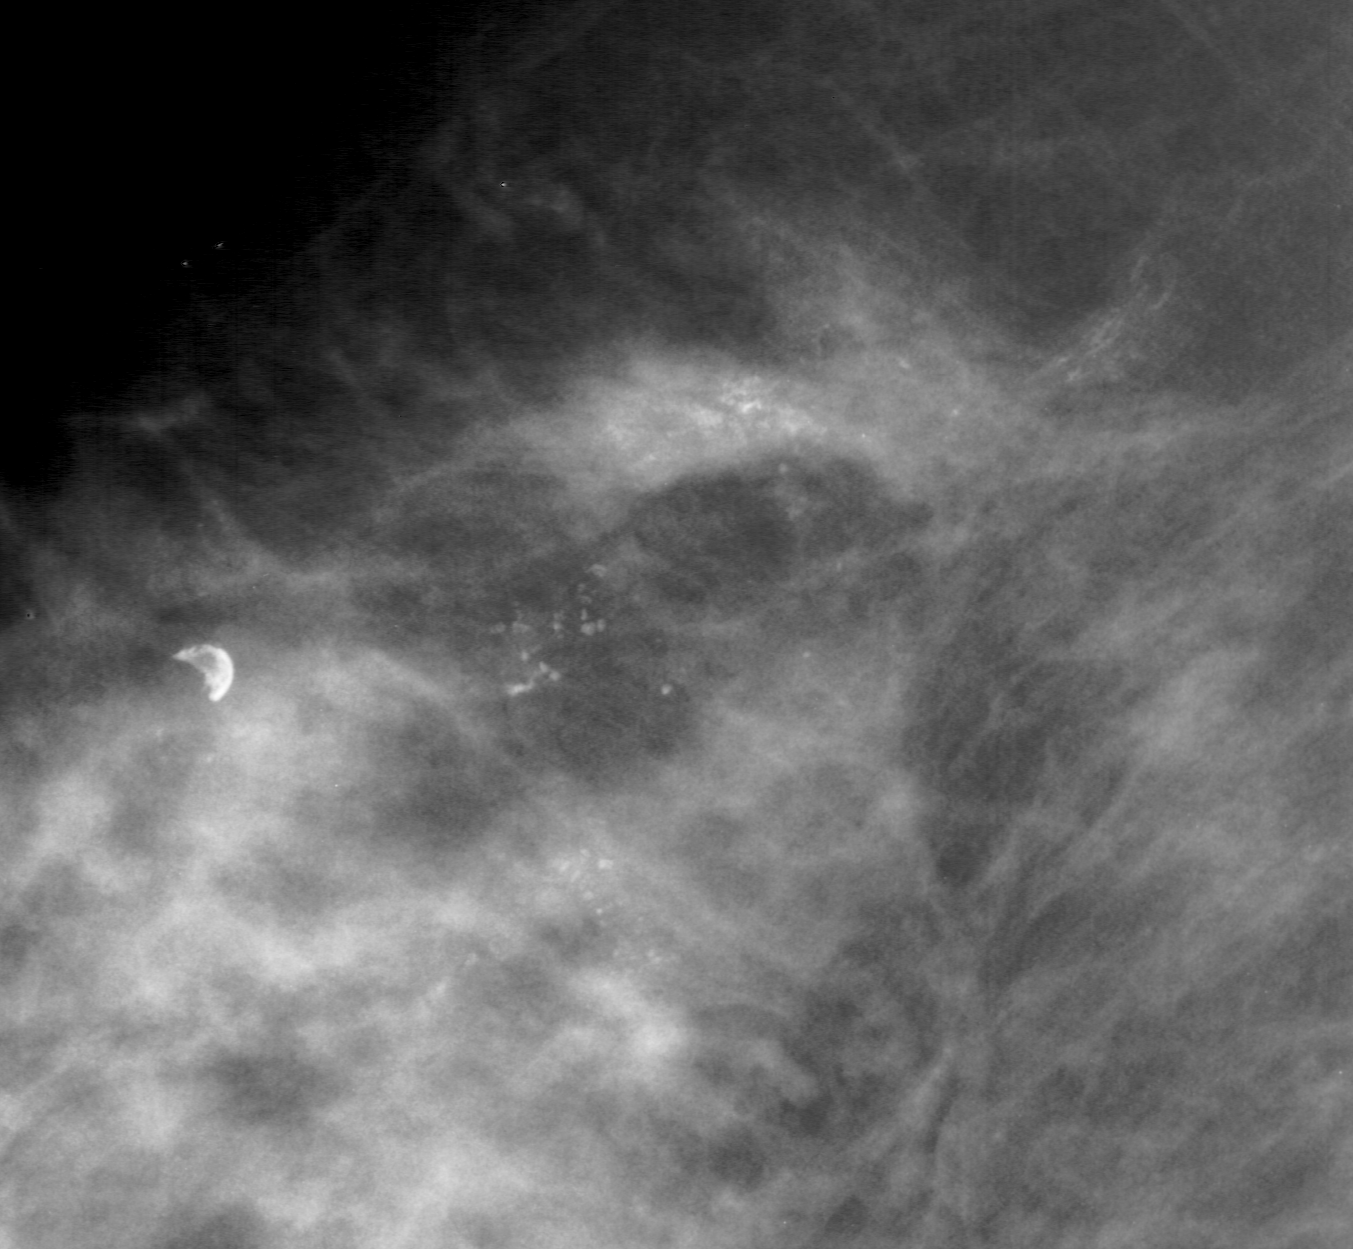
Region of interest cut from a scanned film mammogram (one marked finding); left breast; CC view; BI-RADS breast density category 4 (scale 1–4).
- Finding: calcifications, morphology pleomorphic, distribution regional; BI-RADS assessment category 5; subtlety rating 5 on a 1 (subtle) to 5 (obvious) scale; pathology result (as recorded, not read from the image): malignant.